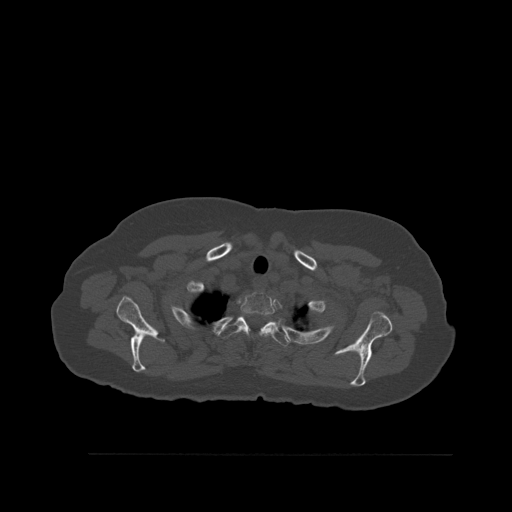
CT including the spine, one axial slice; slice 437 of 527 in the series (ordered by position); bone window (W 1800 / L 400 HU); 1.5 mm slice thickness; 512 × 512 image matrix, field of view 470 × 470 mm. Female patient, age 73 years. Case-level facts recorded for this patient, not image findings: primary cancer: breast.
Structures marked on this image (semi-automatic segmentation, software-assisted and operator-edited):
- T1 vertebra: box from (x=240, y=291) to (x=275, y=332) px
- T2 vertebra: (x=217, y=312)–(x=291, y=347)